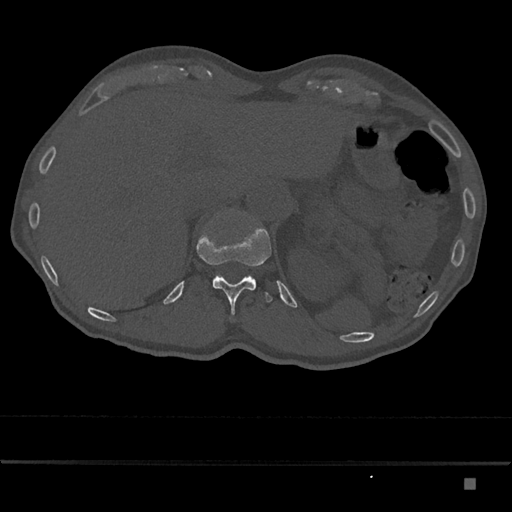
CT including the spine, one axial slice. Position 605 of 797 along the scan axis. Reconstruction kernel Br40s/3. Bone window (W 1800 / L 400 HU). 0.5 mm slice thickness. 512 × 512 image matrix. Male patient, age 72 years. From the clinical record (not read from this slice): primary cancer: prostate.
Annotated regions visible in this slice (semi-automatic segmentation, software-assisted and operator-edited):
- T12 vertebra: bounding box [x1, y1, x2, y2] px = [197, 227, 272, 315]